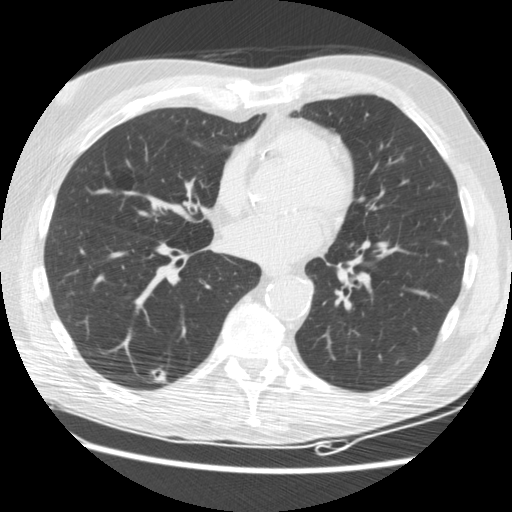
Low-dose screening chest CT, one axial slice. Position 79 of 176 along the scan axis. Reconstruction kernel STANDARD. 120 kVp. Lung window (W 1500 / L -600 HU). 2.5 mm slice thickness. 512 × 512 image matrix, field of view 347 × 347 mm.
Annotated regions visible in this slice (outlined manually by an expert reader):
- lesion 2 (tumor, lower lobe of right lung): bounding box [x1, y1, x2, y2] px = [153, 367, 166, 383]